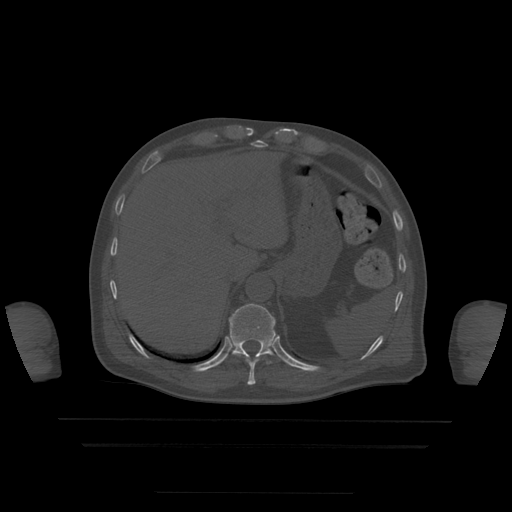
CT including the spine, one axial slice. Position 228 of 522 along the scan axis. Bone window (W 1800 / L 400 HU). 512 × 512 image matrix, field of view 436 × 436 mm. Patient age 68 years. From the clinical record (not read from this slice): primary cancer: urothelial.
Annotated regions visible in this slice (semi-automatic segmentation, software-assisted and operator-edited):
- T10 vertebra: box from (x=233, y=354) to (x=267, y=386) px
- T11 vertebra: (x=229, y=304)–(x=277, y=358)